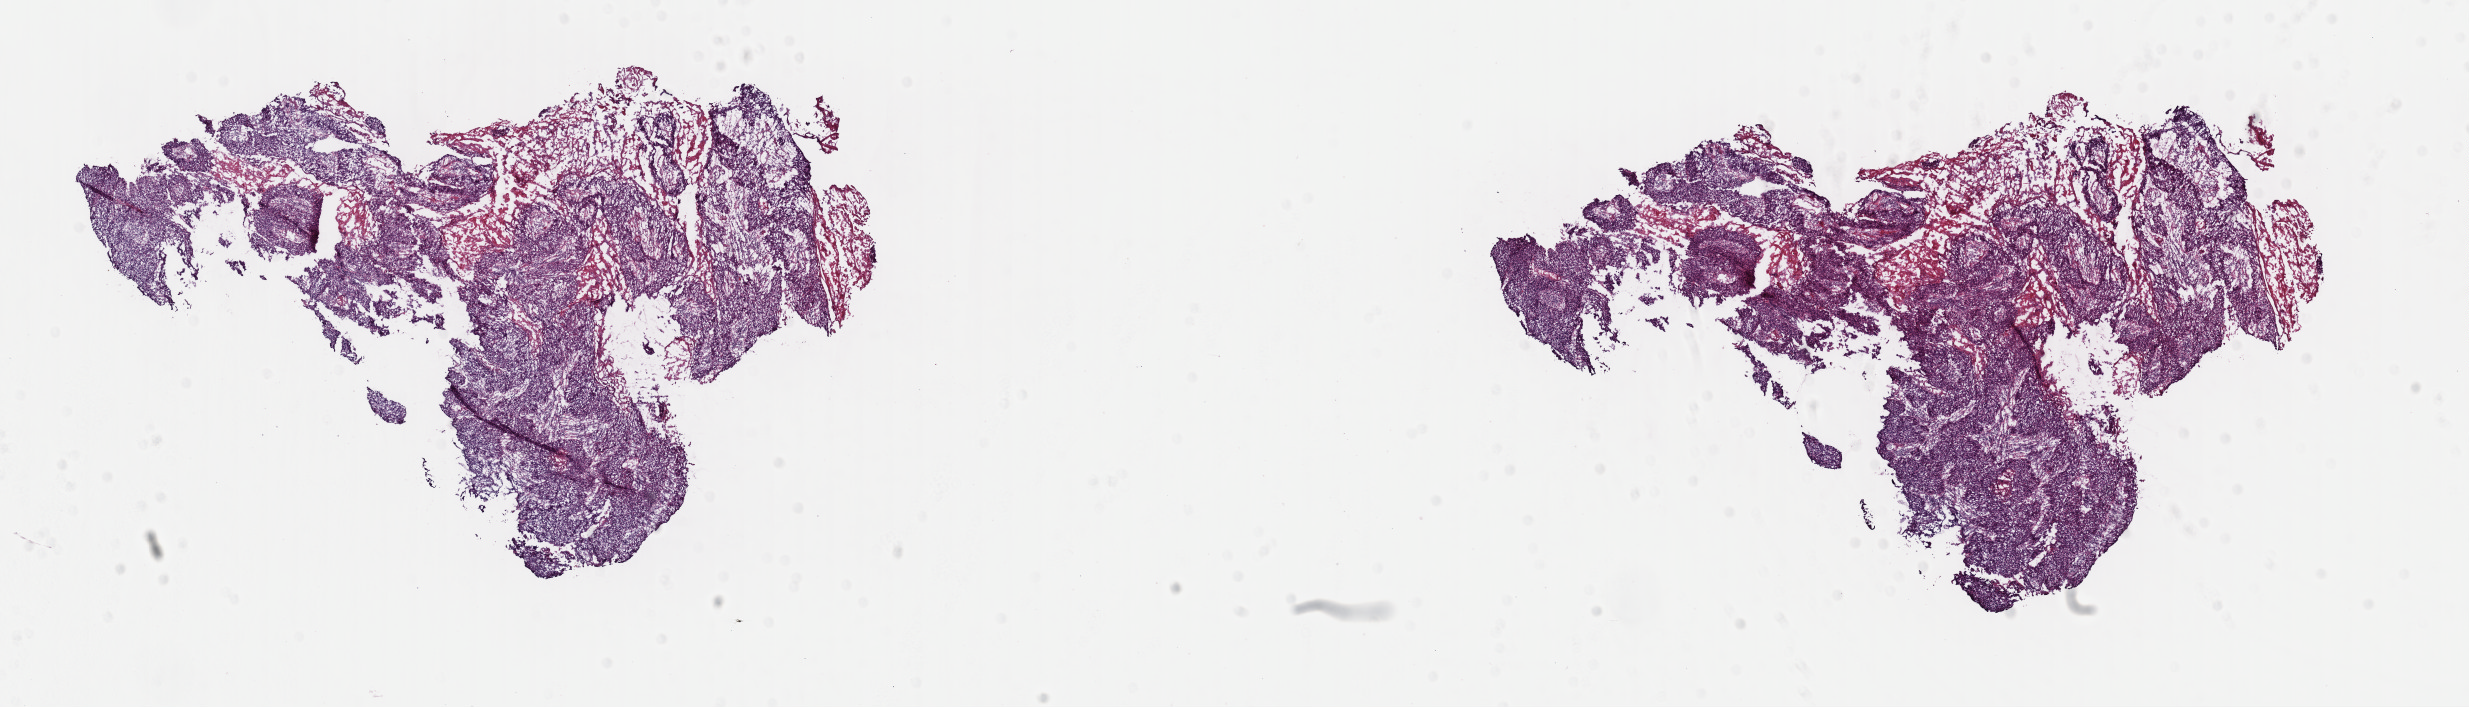
Digitized Hematoxylin and eosin (H&E) stained tissue section (whole slide) — low-resolution overview of the scanned area, about 19.5 x 5.6 mm (slide scanned at 40x). Frozen section. Primary tumour sample from the cervix. Female, age 51 years at initial diagnosis. Histologic grade: G3 (poorly differentiated). Composition of this section per pathologist review: tumour cells 75%, tumour nuclei 85%, normal cells 0%, stromal cells 10%, necrosis 5%. Inflammatory infiltration, as recorded: lymphocyte infiltration 8%, monocyte infiltration 1%, neutrophil infiltration 1%.
FIGO stage: IB1. Histologic diagnosis: Squamous cell carcinoma, keratinizing, NOS (cervix uteri).